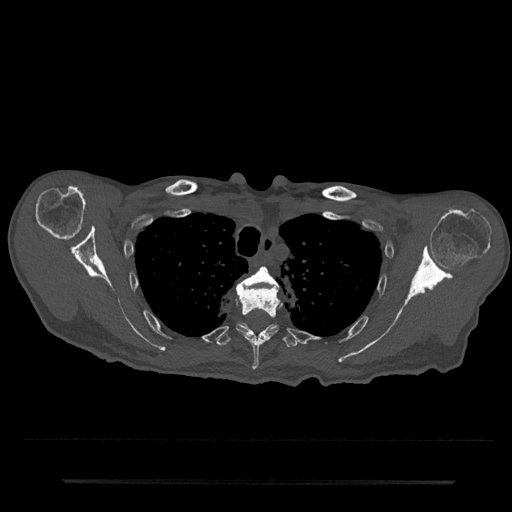
CT including the spine, one axial slice; slice 614 of 797 in the series (ordered by position); reconstruction kernel Br40s/3; 120 kVp; bone window (W 1800 / L 400 HU); 0.5 mm slice thickness; 512 × 512 image matrix. Male patient, age 74 years. Case-level facts recorded for this patient, not image findings: primary cancer: prostate.
Annotated regions visible in this slice (semi-automatic segmentation, software-assisted and operator-edited):
- T3 vertebra: bounding box <238,266,280,290> (left, top, right, bottom; pixels)
- T4 vertebra: <236,286,282,370>
- T5 vertebra: <215,322,299,348>